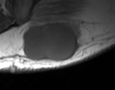
MRI of an extremity soft-tissue mass, one axial slice; position 19 of 35 along the scan axis; MR volume resampled by the dataset authors to the PET/CT grid (not the native acquisition matrix); 115 × 90 image matrix, field of view 112 × 88 mm. Male patient. Case-level facts recorded for this patient, not image findings: histological type: pleiomorphic leiomyosarcoma; grade: high; site of the primary tumour: left buttock.
Structures marked on this image (expert contour drawn on MRI and transferred to this co-registered scan by the dataset authors):
- gross tumour volume including surrounding oedema: bounding box (x1, y1, x2, y2) in pixels: (24, 21, 82, 61)
- gross tumour volume (mass): (24, 21, 81, 61)